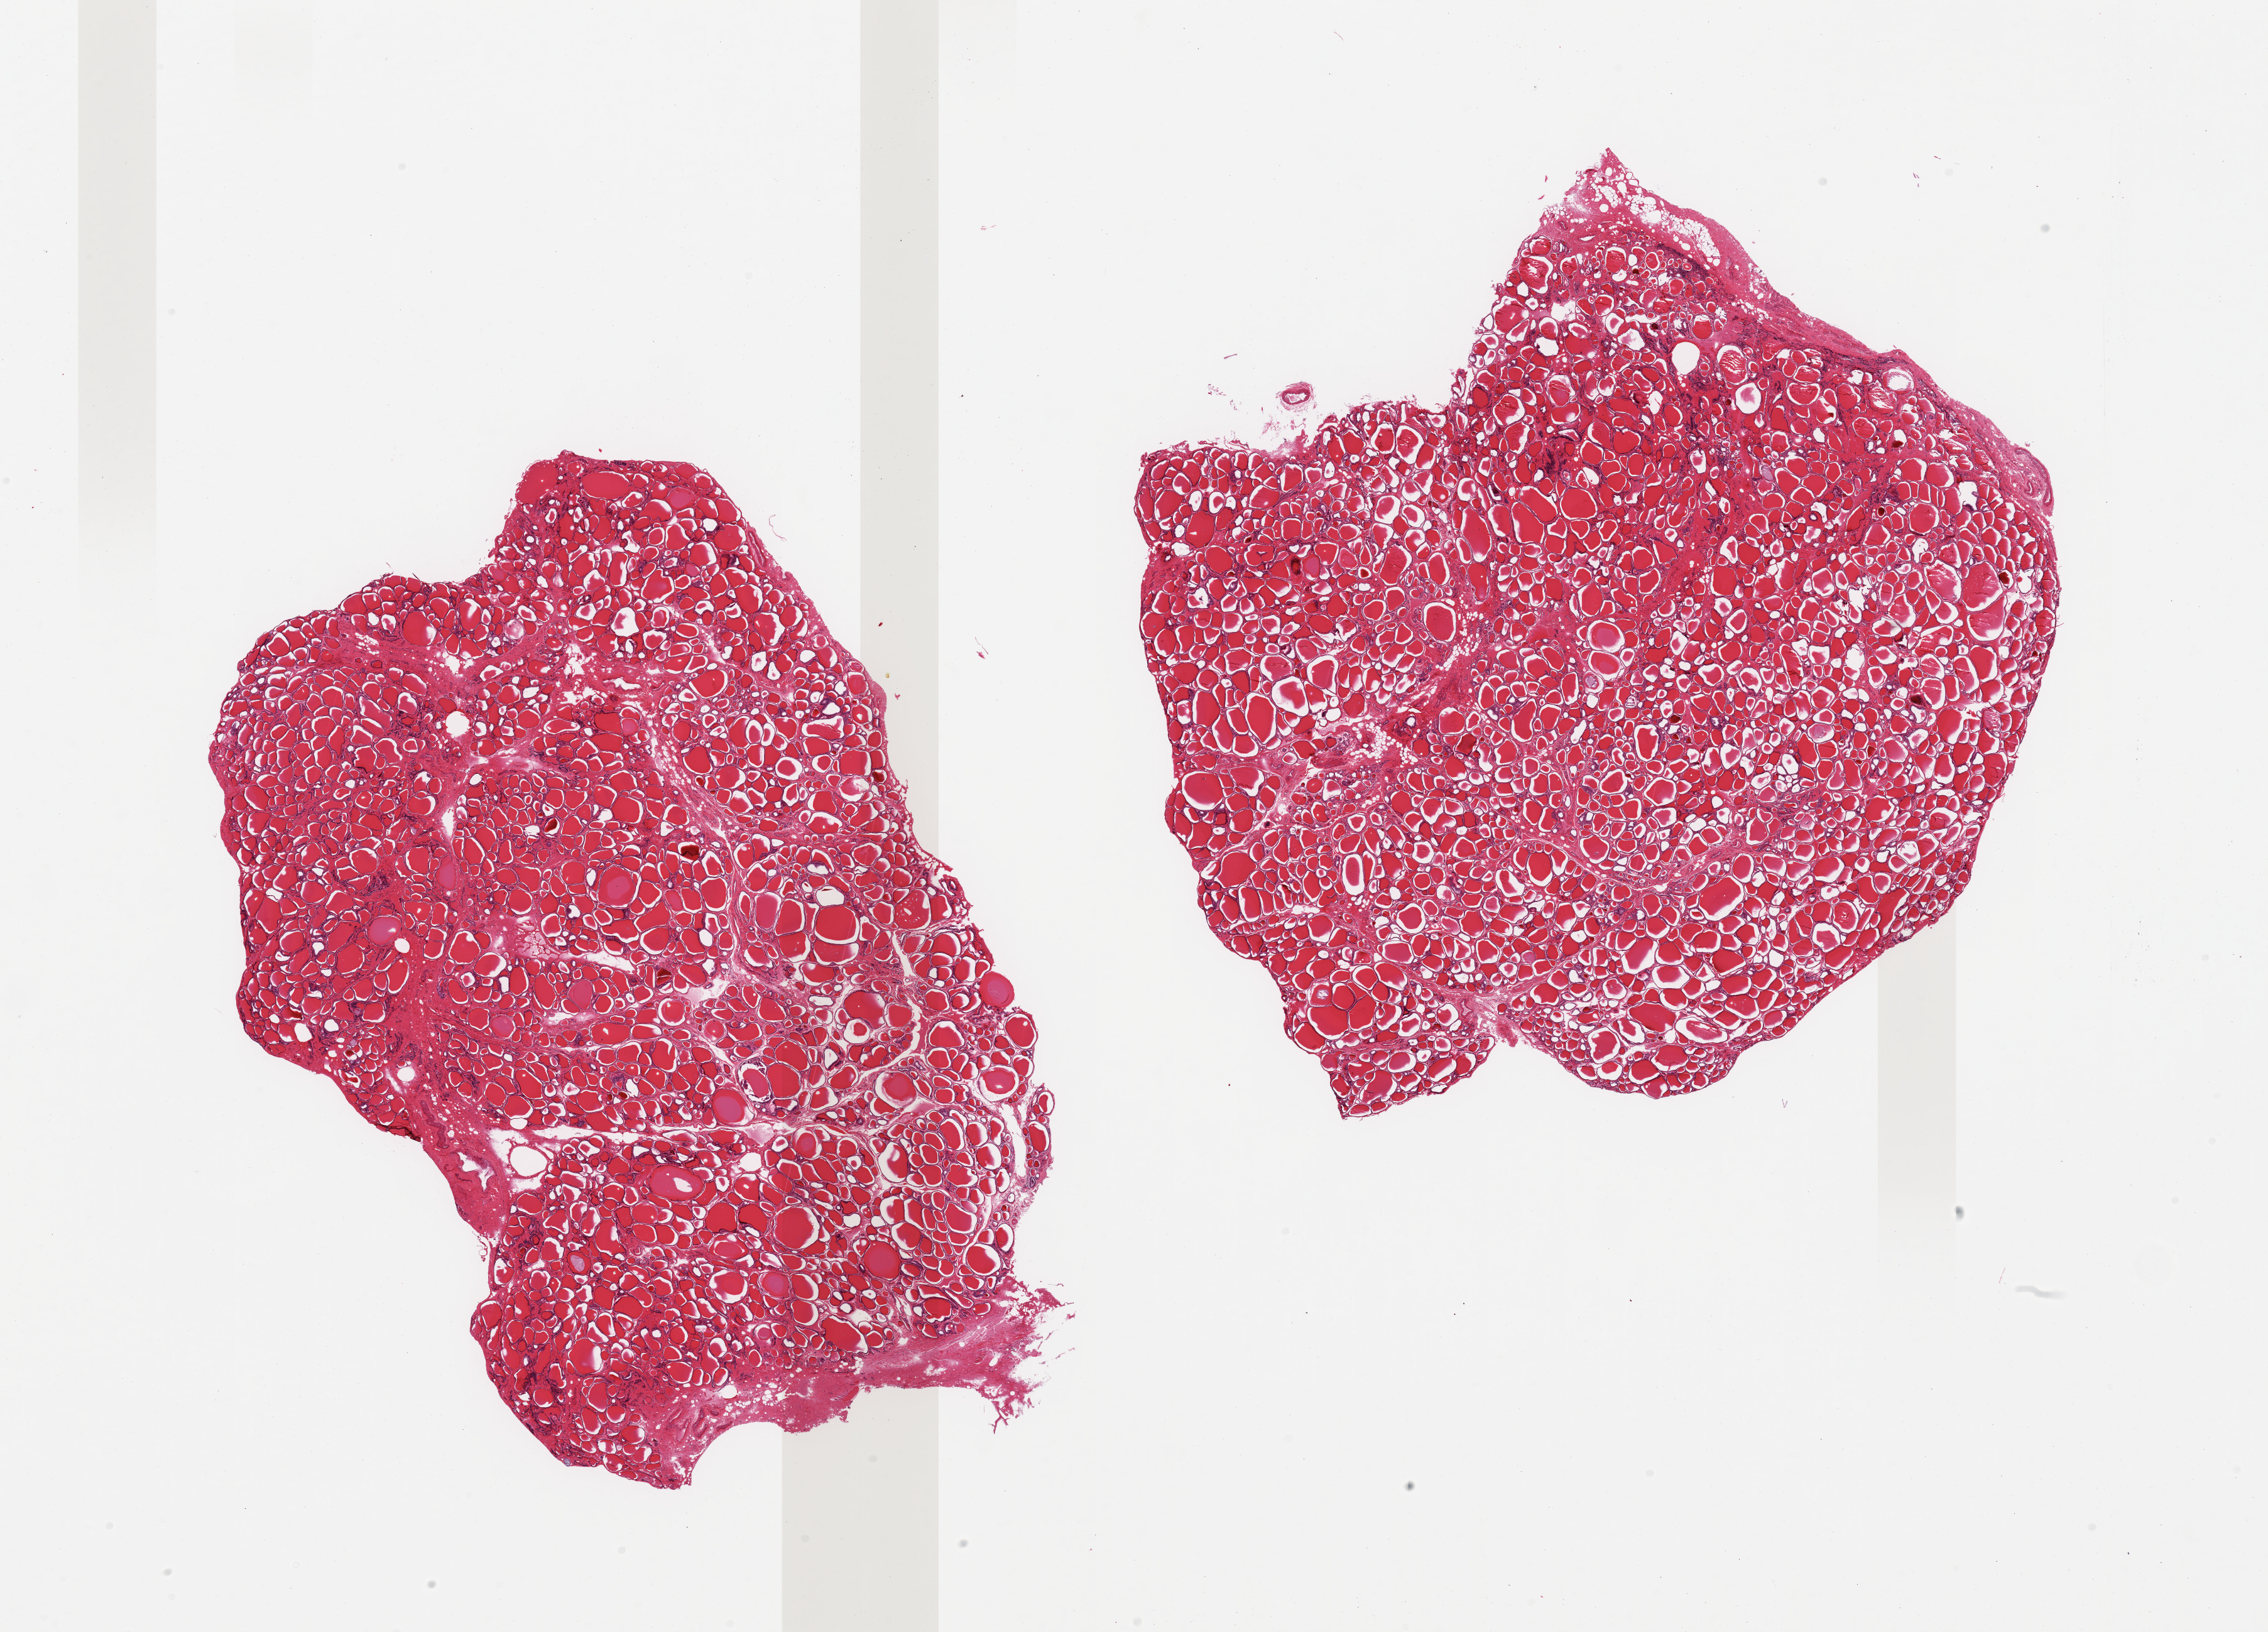
Digitized haematoxylin and eosin-stained section — low-resolution overview of the scanned area, about 28.5 x 20.5 mm, PAXgene-fixed paraffin-embedded (PFPE) section, section of thyroid (target tissue), tissue donor sample. Donor sex: male.
Pathologist's review note for this sample: 2 pieces; discrete accentuation of interstitial fibrous tissue with subtle micronodularity.